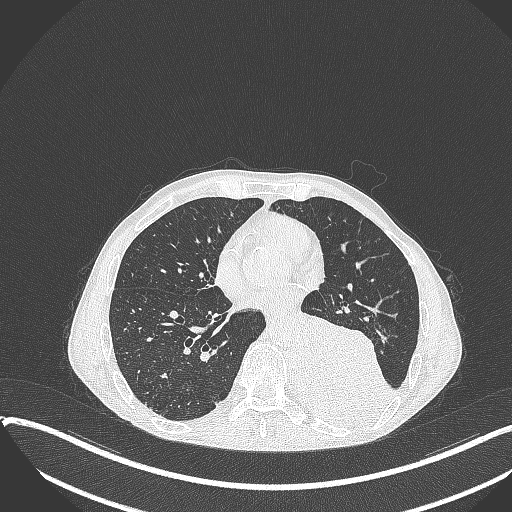
Chest CT, one axial slice. Position 152 of 401 along the scan axis. 120 kVp. Lung window (W 1500 / L -600 HU). 1 mm slice thickness. 512 × 512 image matrix. Male patient, age 57 years. Case-level facts recorded for this patient, not image findings: clinical TNM (as recorded): T4 N0 M0.
Structures marked on this image (rectangle marked by the reading radiologist):
- lung tumour (recorded histology: squamous cell carcinoma): bounding box [x1, y1, x2, y2] px = [294, 308, 391, 425]